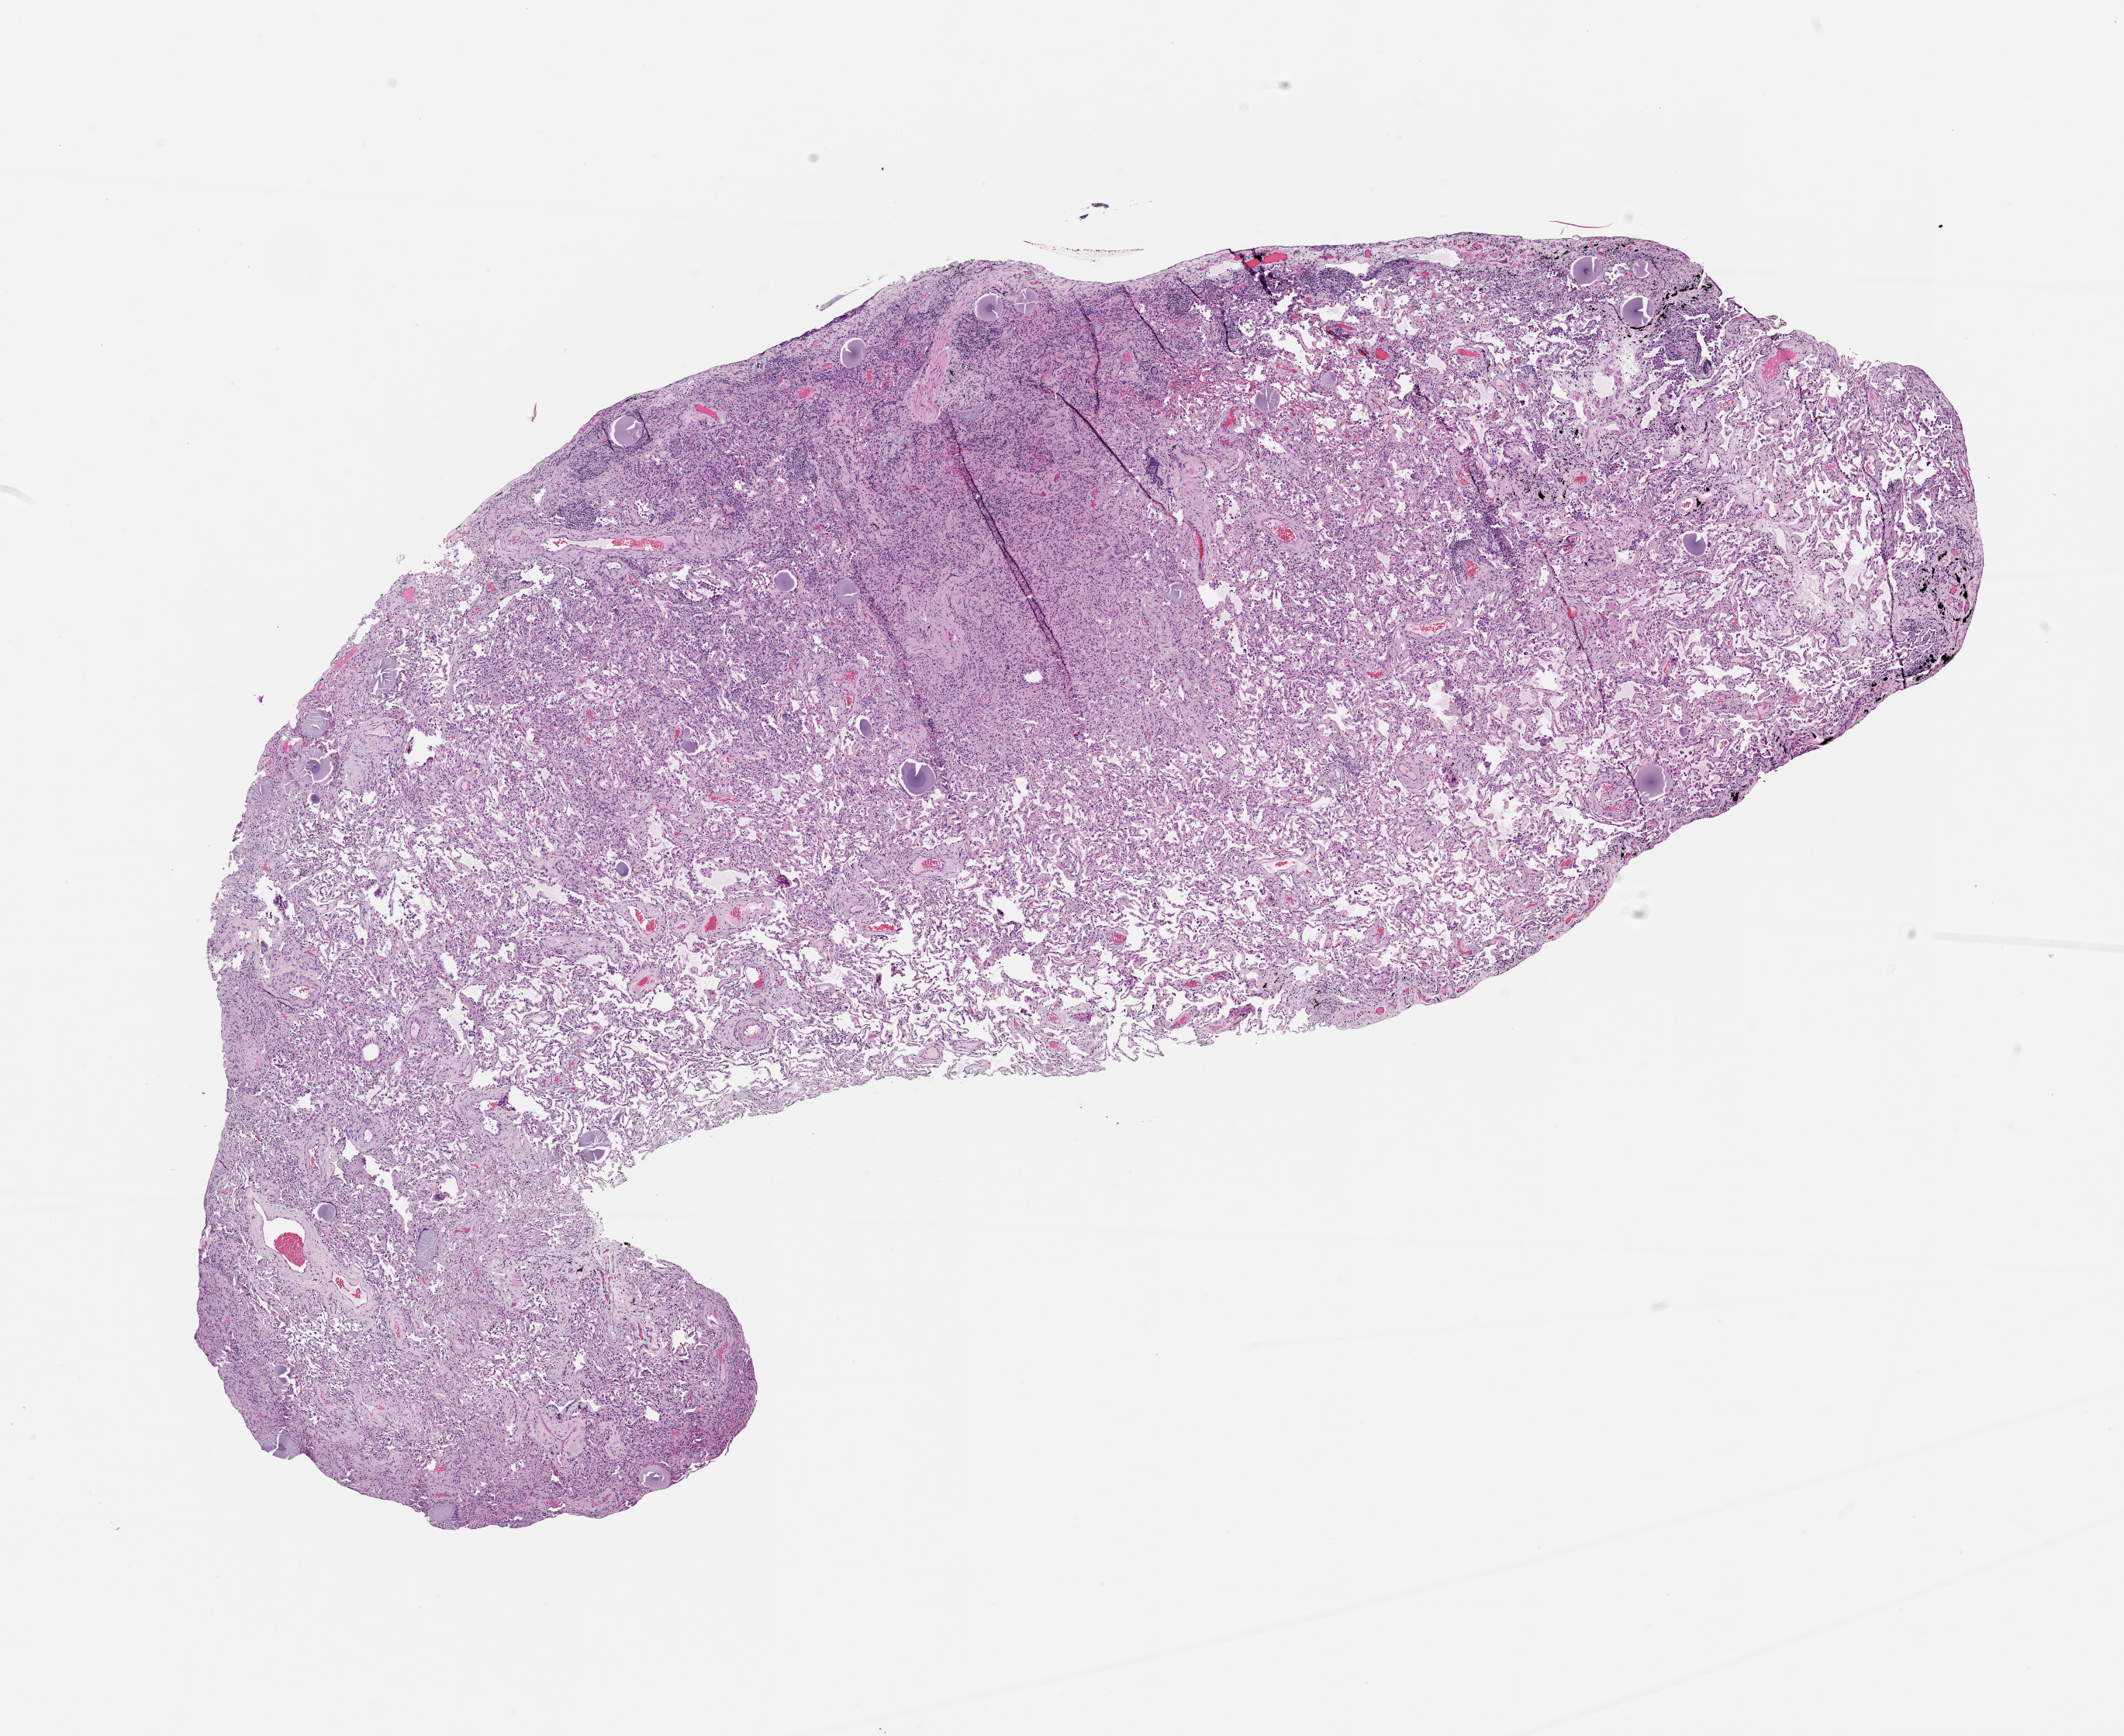
H&E-stained whole-slide image, low-resolution overview of the scanned area, about 11.0 x 9.0 mm (from a 20x scan); lung, normal (non-tumour) tissue. Female, 82 y/o.
This section: normal (non-tumour) tissue from the same patient. Patient diagnosis (cohort enrolment): squamous cell carcinoma (lung).